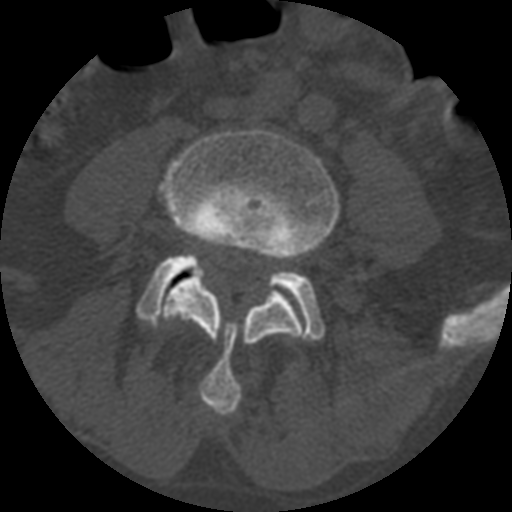
CT including the spine, one axial slice. Position 272 of 399 along the scan axis. Bone window (W 1800 / L 400 HU). 512 × 512 image matrix. Patient age 71 years. Case-level facts recorded for this patient, not image findings: primary cancer: prostate.
Structures marked on this image (semi-automatic segmentation, software-assisted and operator-edited):
- L4 vertebra: bounding box <158,128,341,416> (left, top, right, bottom; pixels)
- L5 vertebra: <137,251,324,340>